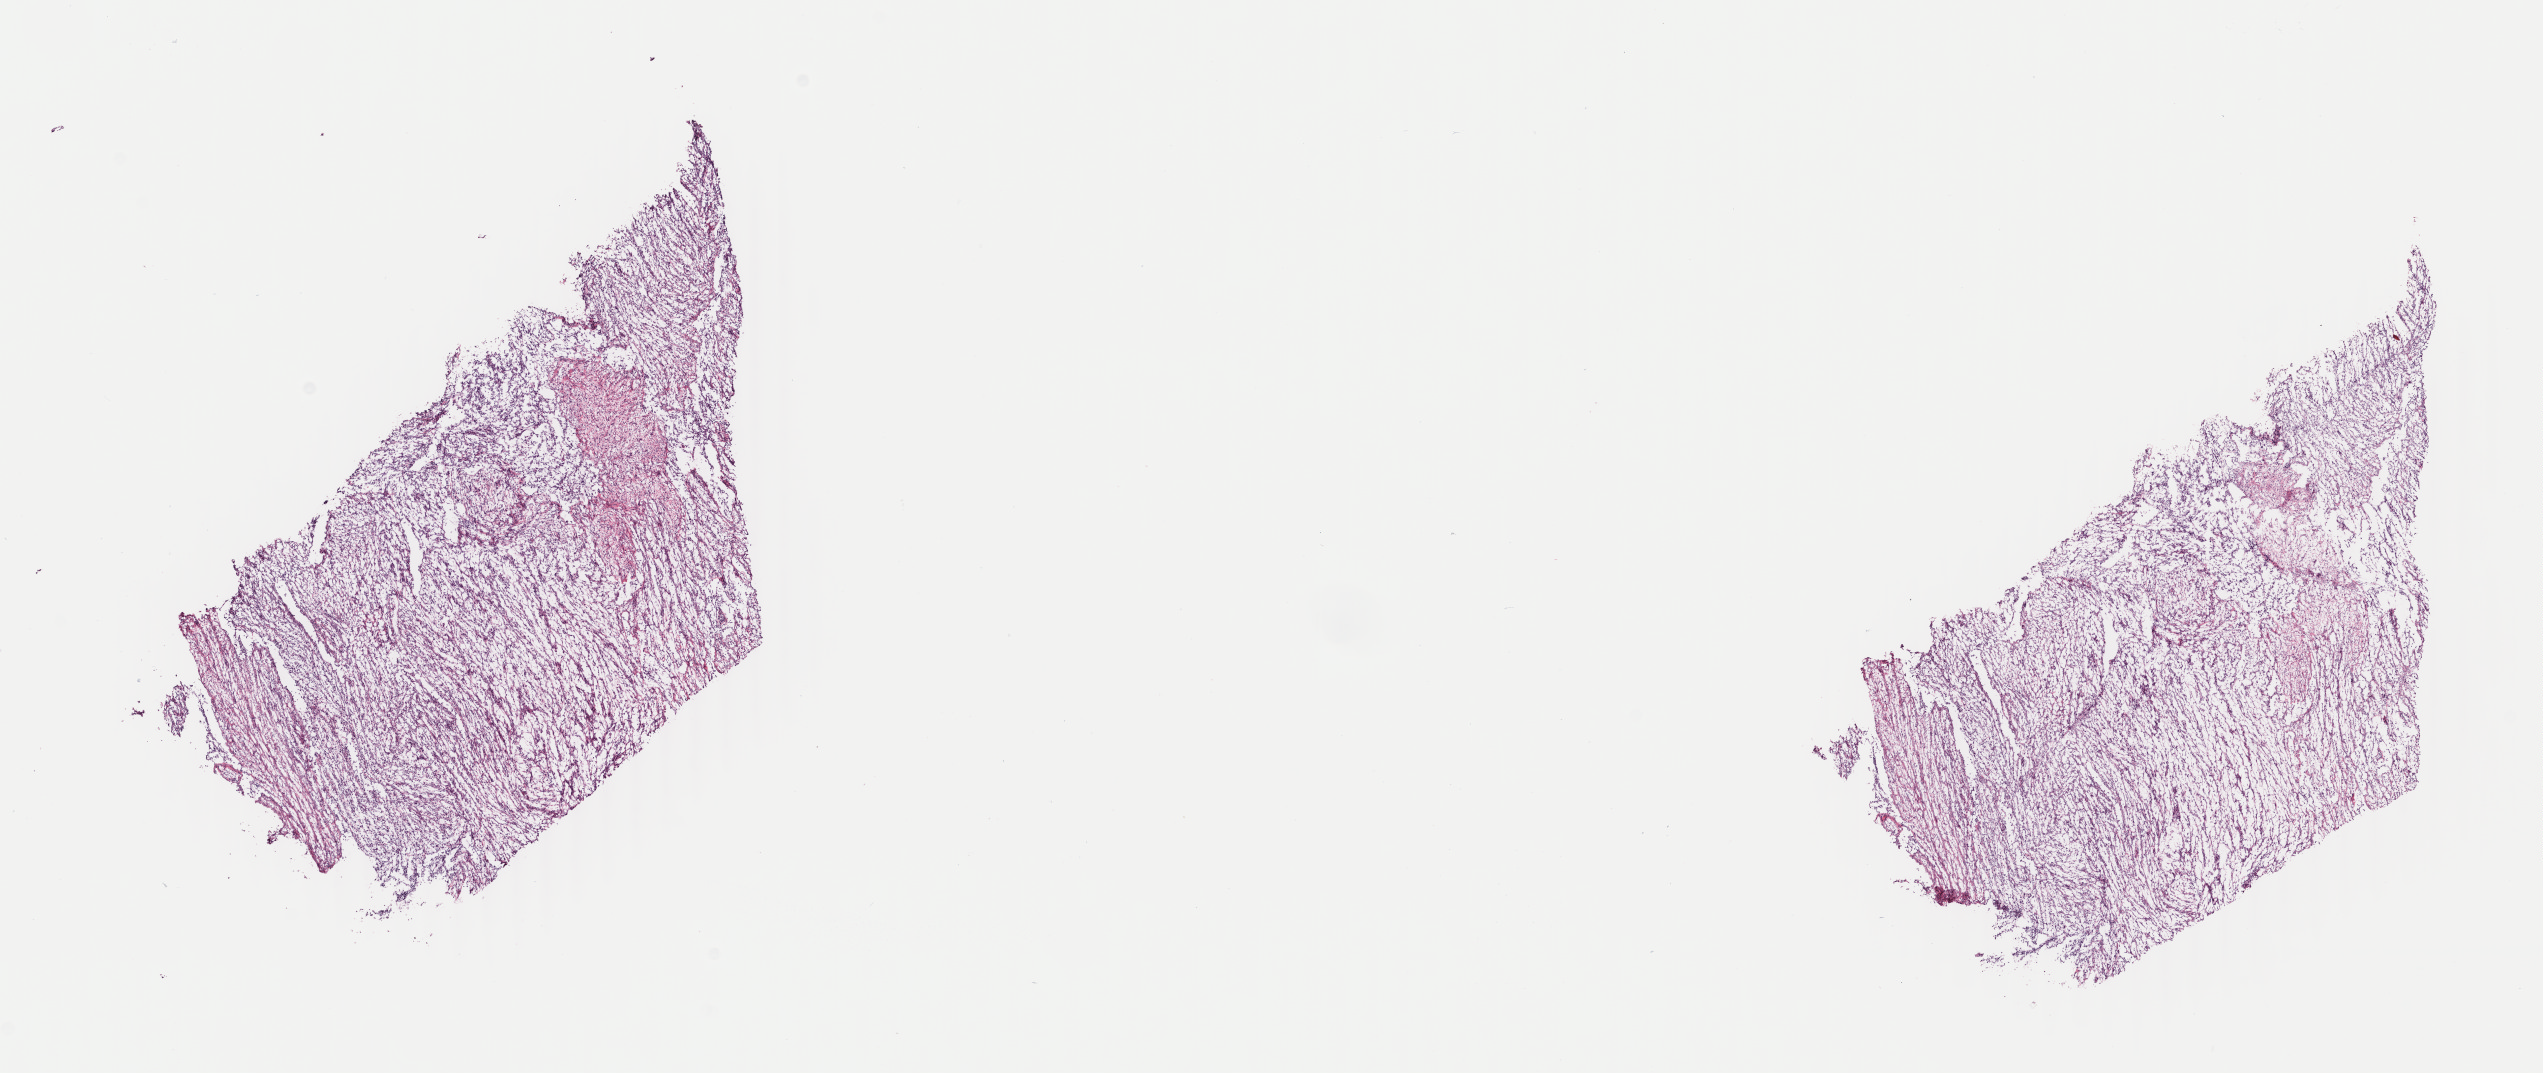
Digitized H&E tissue section (whole slide), shown as a low-resolution overview of the whole scanned area (about 20.2 x 8.5 mm, slide scanned at 40x), frozen section, primary tumour sample from the mesothelium. Male, age 62 years at initial diagnosis. Slide review estimates, as recorded: tumour cells 70%, tumour nuclei 100%, normal cells 0%, stromal cells 30%, necrosis 0%. Inflammatory infiltration, as recorded: lymphocyte infiltration 0%, monocyte infiltration 0%, neutrophil infiltration 0%.
Diagnosis: Epithelioid mesothelioma, malignant (pleura, NOS). AJCC pathologic stage: III (7th edition). TNM: T3 N2 MX.